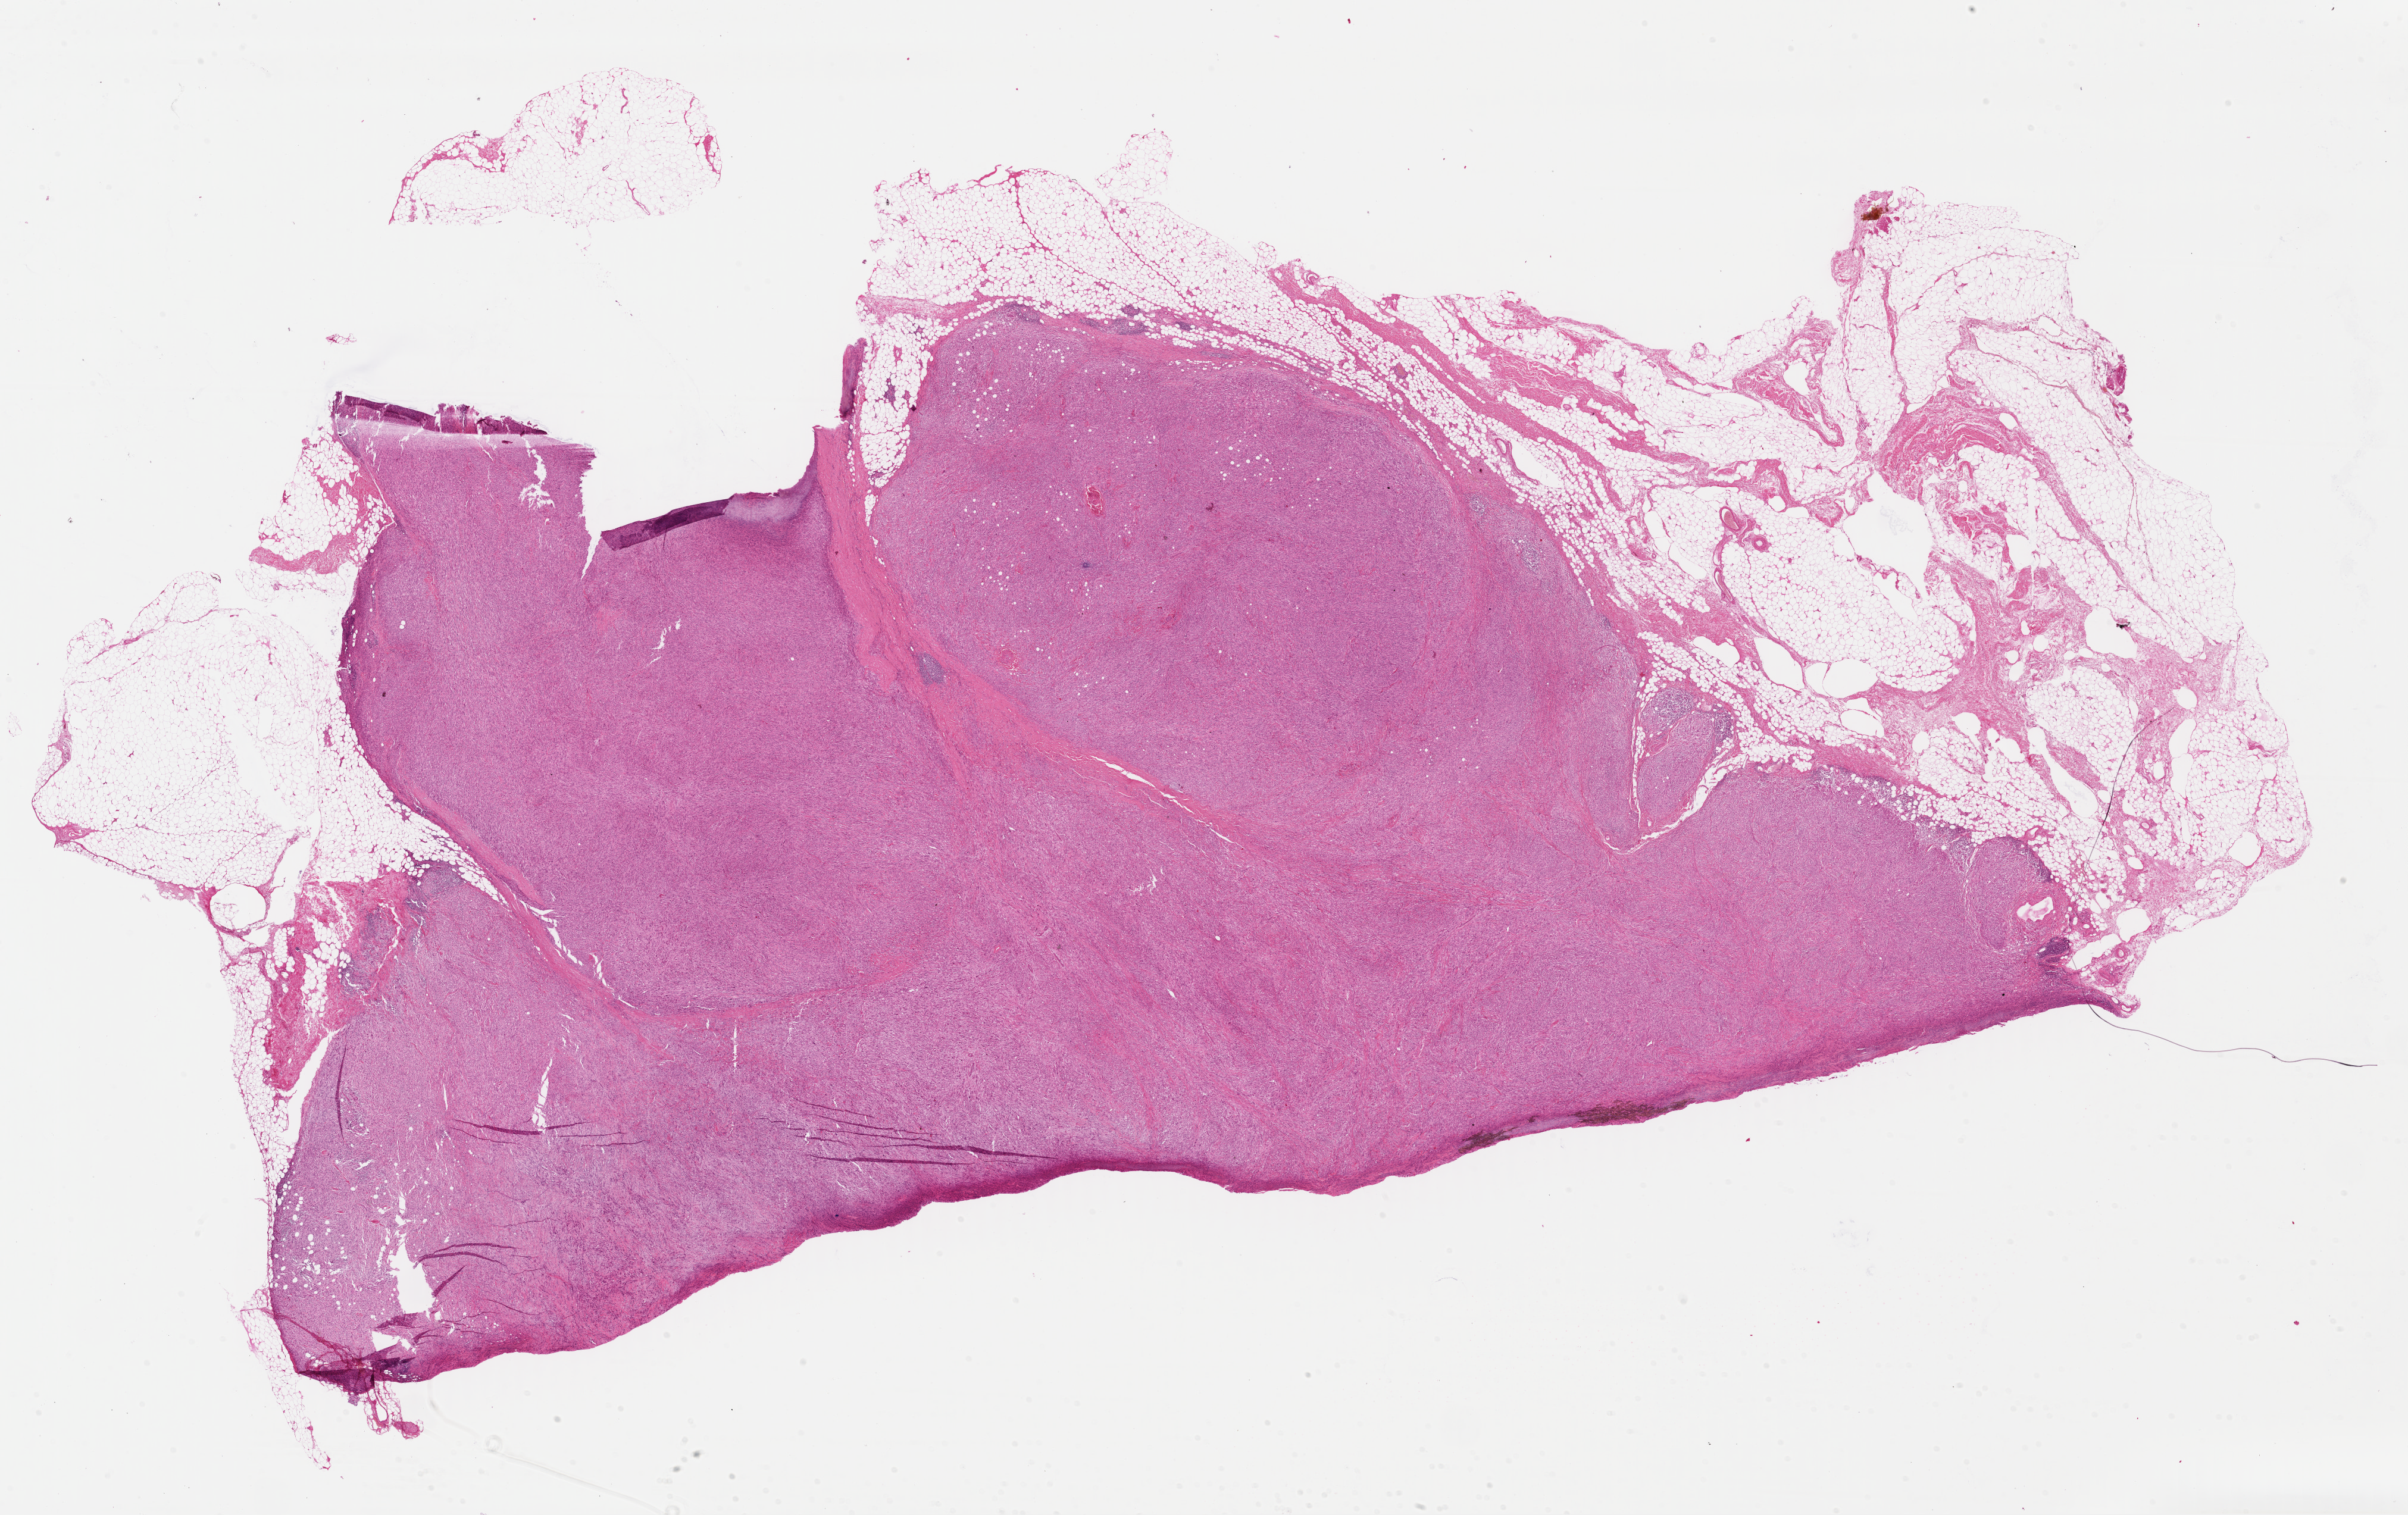
Whole-slide histology image, H&E-stained — a low-resolution overview of the entire scanned area, about 31.8 x 20.0 mm (from a 40x scan); formalin-fixed paraffin-embedded (FFPE) diagnostic section; primary tumour sample from the skin. Male patient; age at initial diagnosis 61 years.
• histologic diagnosis: Malignant melanoma, NOS